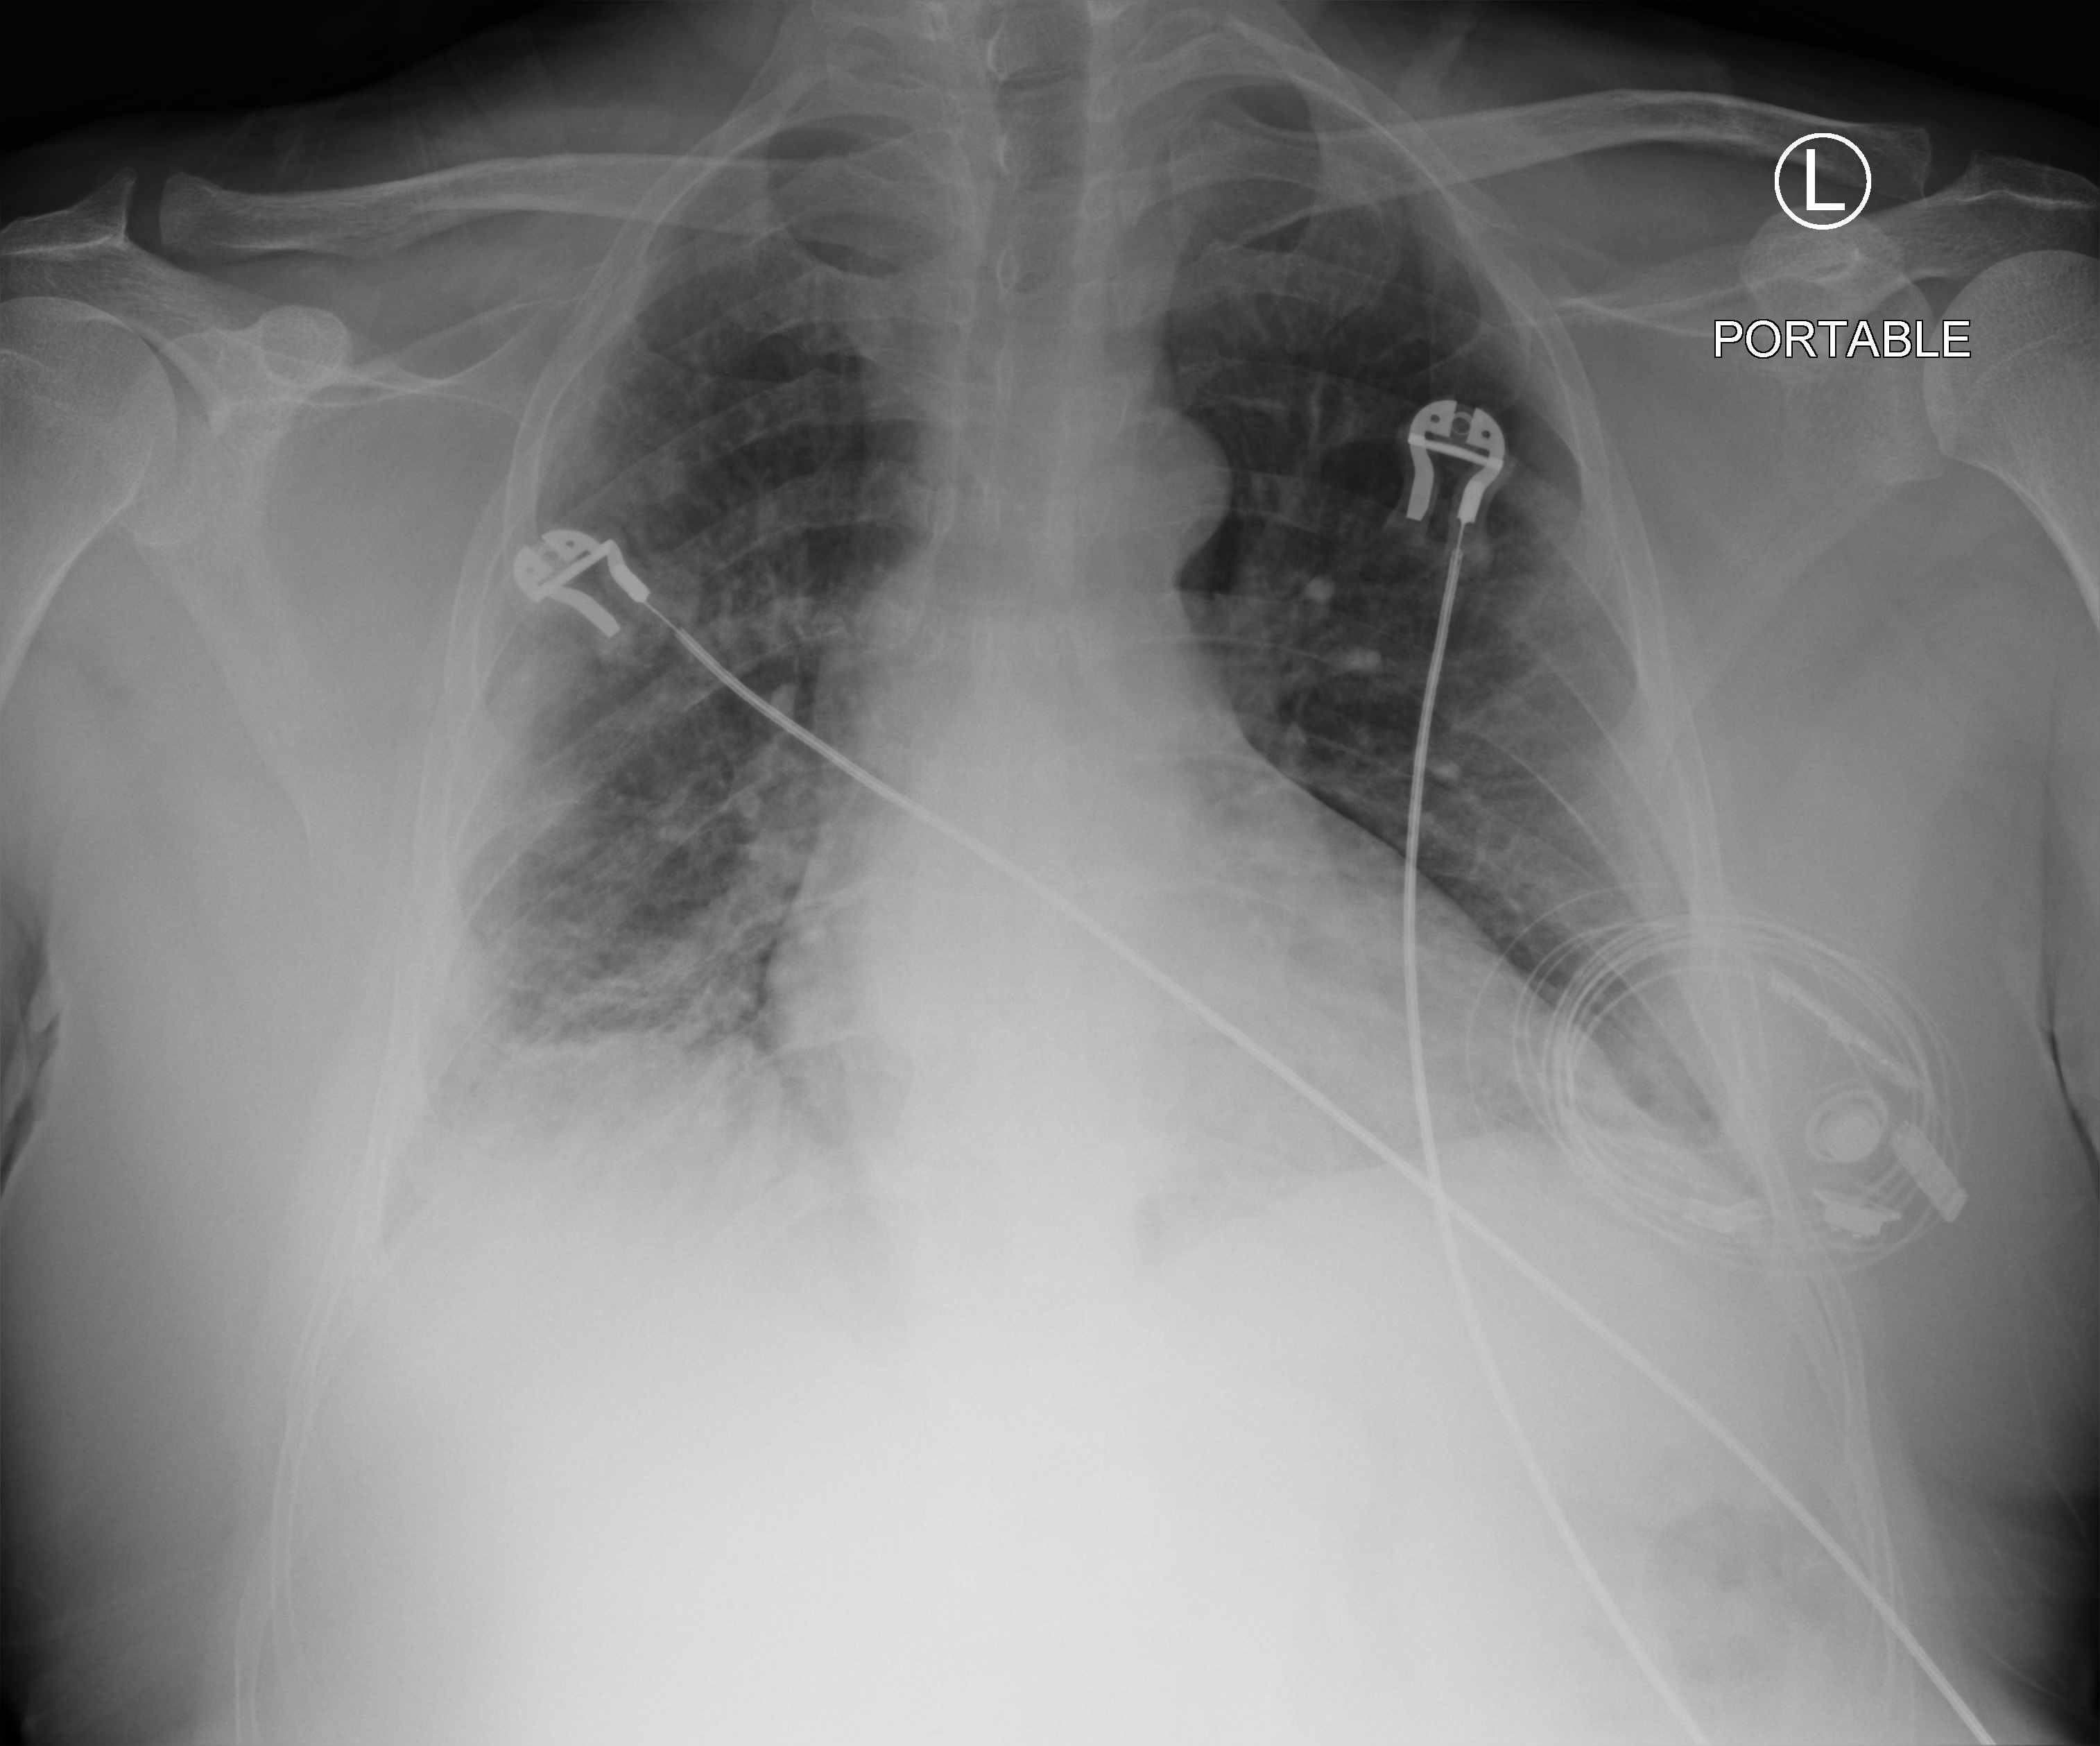
Portable chest radiograph; anteroposterior (AP) projection. Patient hospitalised with COVID-19; male, aged 60–74 years.
Admission-level facts for this patient (not findings on this image; timing relative to this image not recorded): admitted to intensive care during this hospital stay: yes.